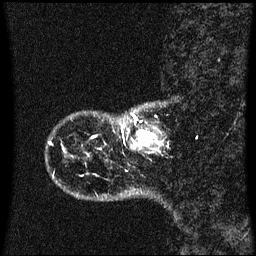
Breast MRI (dynamic contrast-enhanced), one sagittal slice. Slice 7 of 60 in the series (ordered by position). Dynamic contrast-enhanced series, image 2 of 3 at this slice position (ordered by acquisition). 1.5 T. TE 4.2 ms, TR 8.4 ms. 2 mm slice thickness. 256 × 256 image matrix, field of view 220 × 220 mm. Female patient, age 41 years. Case-level facts recorded for this patient, not image findings: setting: breast cancer imaged before/during neoadjuvant chemotherapy; receptor status: triple-negative.
Structures marked on this image (semi-automatic segmentation, software-assisted and operator-edited):
- analysis volume of interest (the breast-tissue region the enhancement analysis was run in; not a lesion): bounding box <120,122,147,145> (left, top, right, bottom; pixels)
- tumour enhancement mask (voxels above the 70 % enhancement threshold inside the analysis volume of interest): <136,132,147,145>